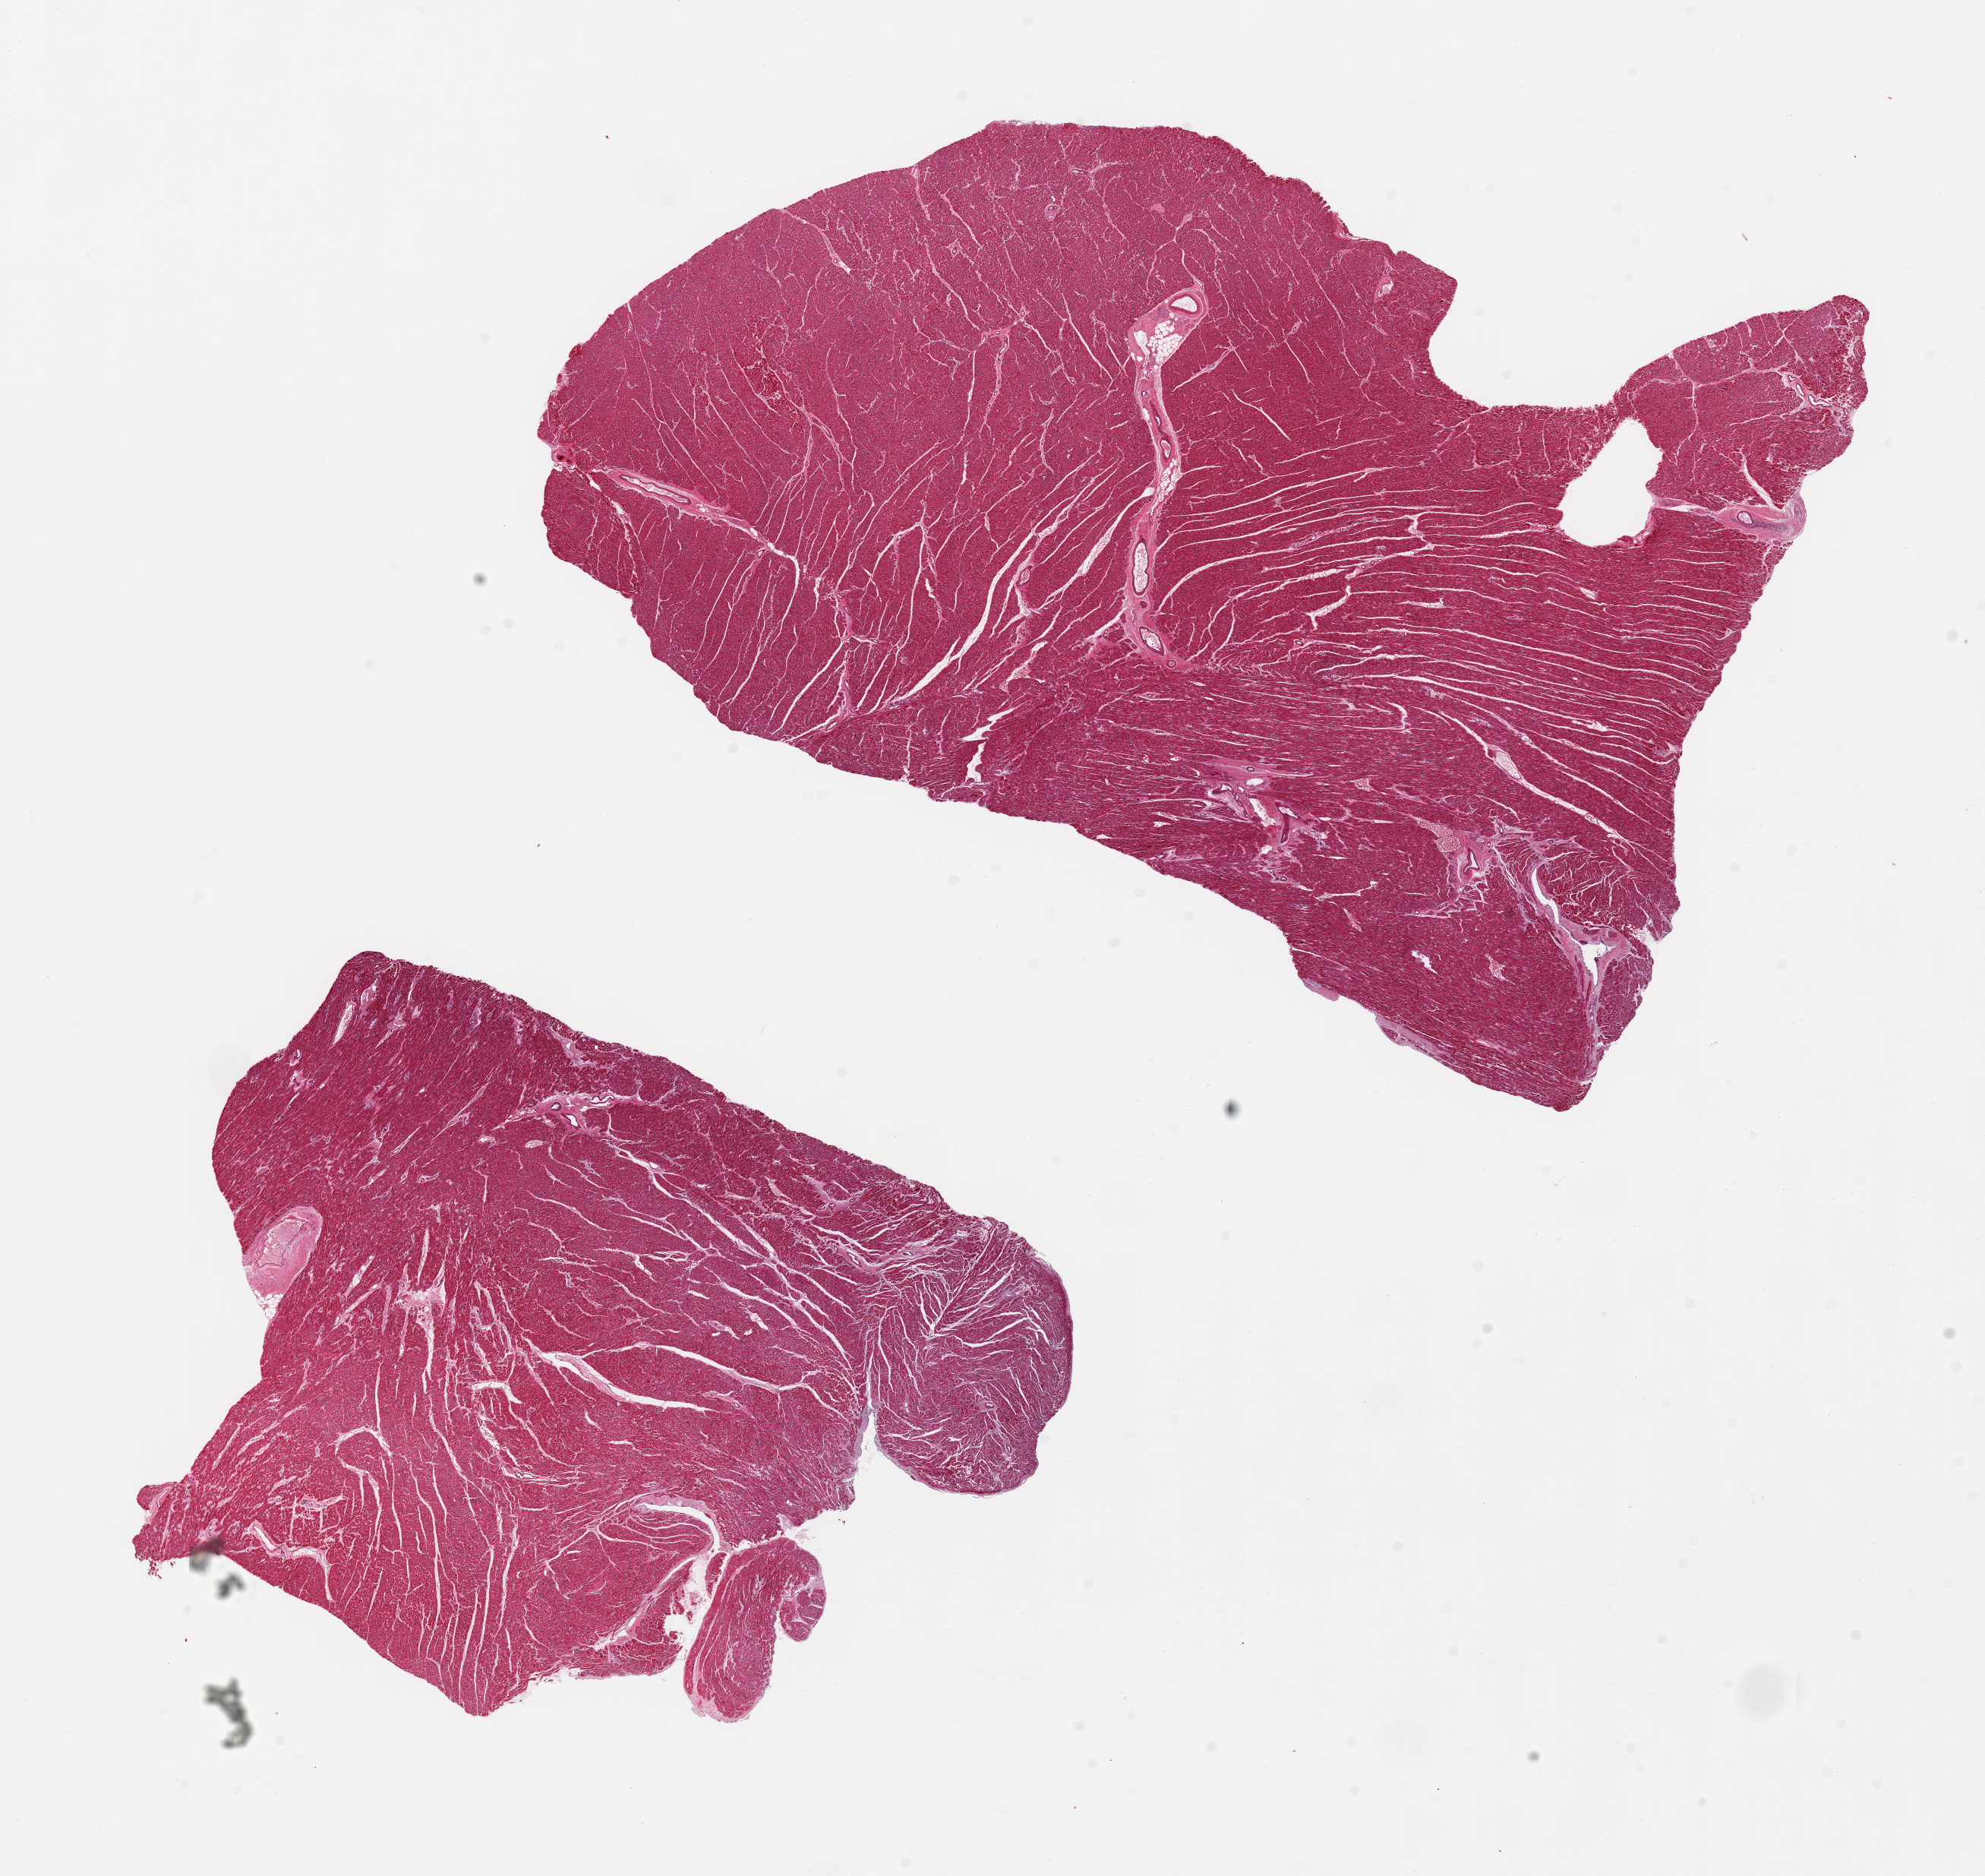
Digitized hematoxylin and eosin (H&E)-stained section, shown as a low-resolution overview of the whole scanned area (about 20.7 x 19.5 mm, slide scanned at 20x); PAXgene-fixed, paraffin-embedded tissue; sampled site (target tissue): heart; tissue donor sample. Donor: female.
- pathologist's review note for this sample: 2 pieces 9x7 & 13x9mm; minimal ischemic changes